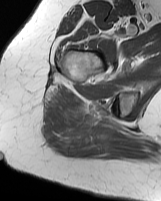
MRI of an extremity soft-tissue mass, one axial slice. Slice 48 of 70 in the series (ordered by position). MR volume resampled by the dataset authors to the PET/CT grid (not the native acquisition matrix). 3.27 mm slice thickness. 161 × 201 image matrix, field of view 157 × 196 mm. Female patient. Case-level facts recorded for this patient, not image findings: histological type: synovial sarcoma; grade: intermediate; site of the primary tumour: right buttock.
Structures marked on this image (expert contour drawn on MRI and transferred to this co-registered scan by the dataset authors):
- gross tumour volume including surrounding oedema: box from (x=72, y=122) to (x=103, y=142) px